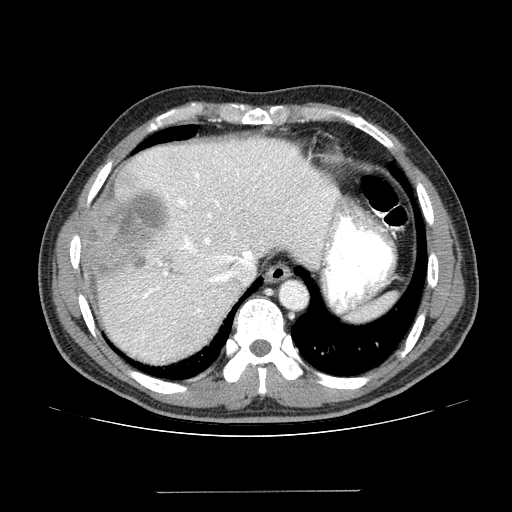
Contrast-enhanced abdominal CT (liver protocol), one axial slice. Position 109 of 131 along the scan axis. 100 kVp. One of 2 acquisitions stored at this slice position. Soft-tissue window (W 400 / L 40 HU). 2.5 mm slice thickness. 512 × 512 image matrix. From the clinical record (not read from this slice): diagnosis: hepatocellular carcinoma (patient treated with transarterial chemoembolisation; whether this scan precedes or follows treatment is not stated here); TNM stage (as recorded): Stage-I; Child-Pugh class: A; tumour nodularity: uninodular.
Outlined on this slice (semi-automatically segmented with operator editing):
- abdominal aorta: bounding box <281,283,306,308> (left, top, right, bottom; pixels)
- liver parenchyma outside the tumour (the mass and vessels are separate outlines, so this box may not span the whole liver): <82,136,338,364>
- mass: <80,189,170,277>
- liver vessels: <130,145,331,355>